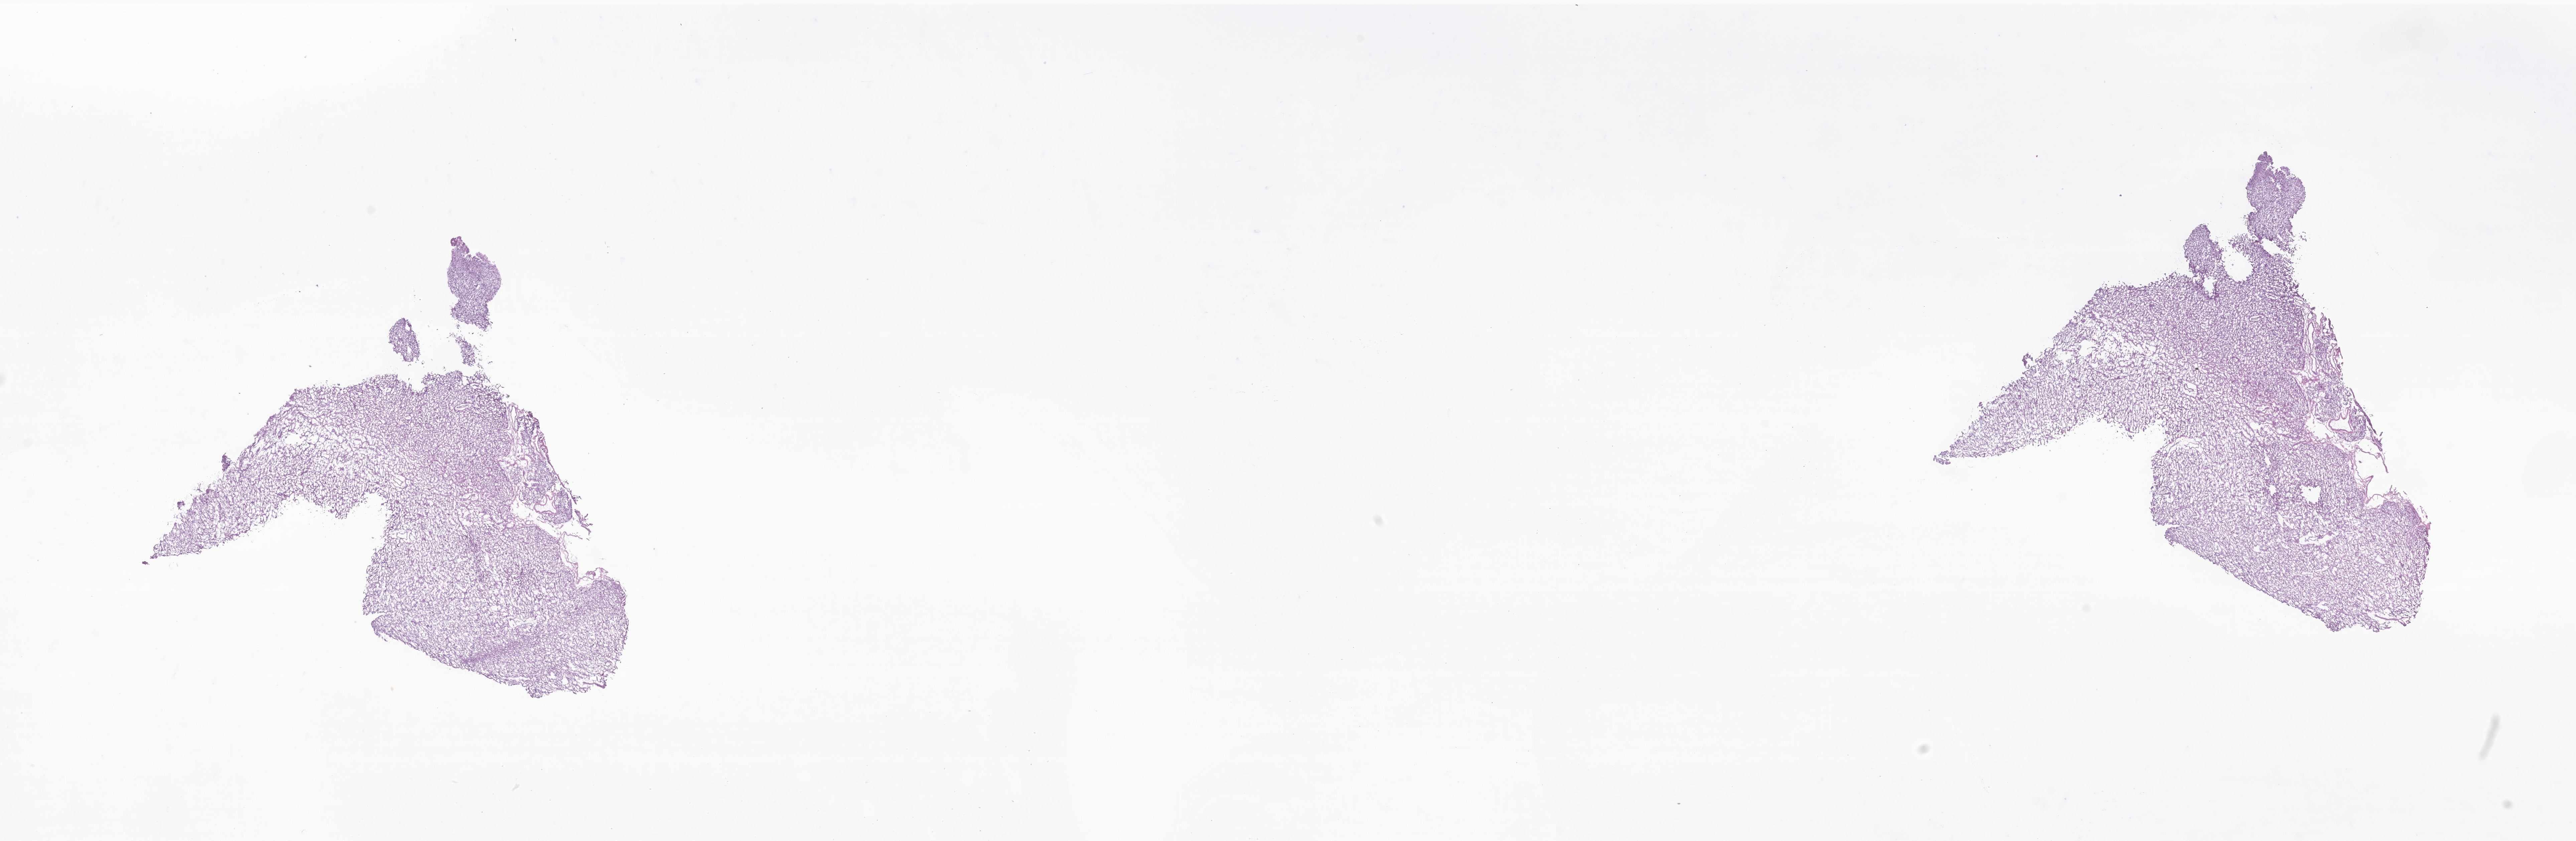
Digitized H&E-stained section of tumor tissue from the brain — whole scanned area (about 32.5 x 10.6 mm) shown as a low-resolution overview. Frozen section. Male patient, age 101 months (8 years 5 months).
• diagnosis: Glioma, malignant